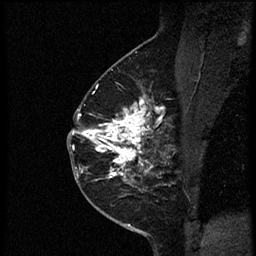
Breast MRI (dynamic contrast-enhanced), one sagittal slice; slice 36 of 56 in the series (ordered by position); dynamic contrast-enhanced study with each time point stored as its own series, time point 2 of 4 at this slice position (early post-contrast, ordered by acquisition time); 1.5 T; TE 4.2 ms, TR 18.9 ms; 2 mm slice thickness; 256 × 256 image matrix, field of view 200 × 200 mm. Female patient. From the clinical record (not read from this slice): setting: breast cancer imaged before/during neoadjuvant chemotherapy; receptor status: HER2-positive.
Structures marked on this image (semi-automatic segmentation, software-assisted and operator-edited):
- analysis volume of interest (the breast-tissue region the enhancement analysis was run in; not a lesion): bounding box <78,86,174,189> (left, top, right, bottom; pixels)
- tumour enhancement mask (voxels above the 100 % enhancement threshold inside the analysis volume of interest): <78,95,170,184>